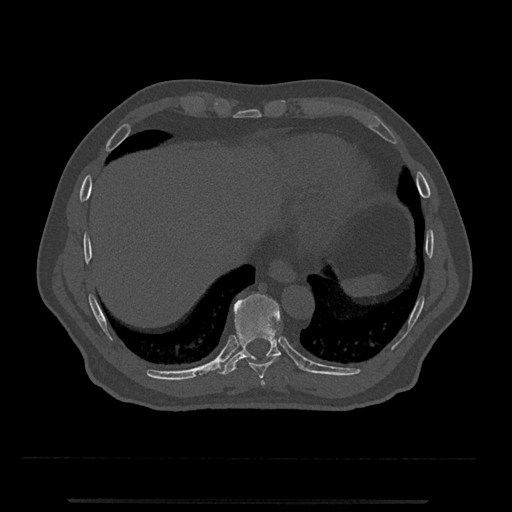
CT including the spine, one axial slice. Position 544 of 797 along the scan axis. 120 kVp. Bone window (W 1800 / L 400 HU). 512 × 512 image matrix. Male patient, age 63 years. From the clinical record (not read from this slice): primary cancer: prostate.
Outlined on this slice (semi-automatically segmented with operator editing):
- T10 vertebra: box from (x=218, y=293) to (x=281, y=375) px
- T8 vertebra: (x=261, y=380)–(x=265, y=386)
- T9 vertebra: (x=249, y=355)–(x=281, y=379)